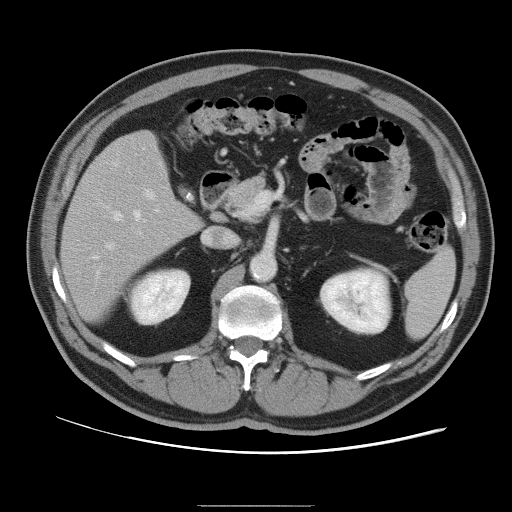
Contrast-enhanced abdominal CT, one axial slice. Slice 51 of 105 in the series (ordered by position). Soft-tissue window (W 400 / L 40 HU). 5 mm slice thickness. 512 × 512 image matrix, field of view 399 × 399 mm. Male patient, age 64 years. From the clinical record (not read from this slice): diagnosis: colorectal cancer liver metastases, imaged before liver resection; multiple liver metastases: yes; largest metastasis: 3 cm; chemotherapy before resection: yes.
Outlined on this slice (outlined manually by an expert reader):
- hepatic veins: bounding box <94,210,145,275> (left, top, right, bottom; pixels)
- liver: <63,131,201,321>
- planned liver remnant (the part of the liver to remain after resection): <63,131,201,322>
- portal vein (with intrahepatic branches): <105,189,155,250>